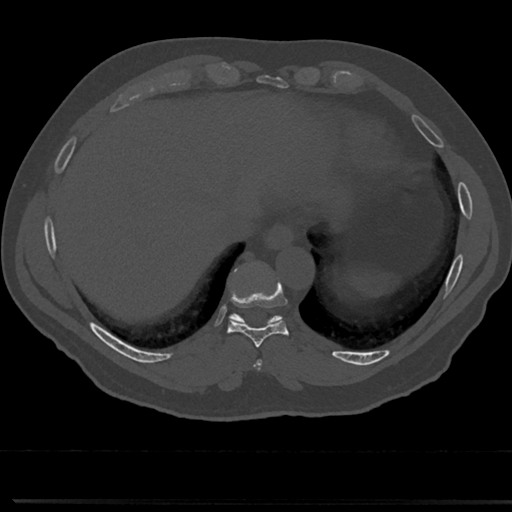
CT including the spine, one axial slice. Position 294 of 817 along the scan axis. Bone window (W 1800 / L 400 HU). 512 × 512 image matrix, field of view 355 × 355 mm. Patient: male, 61 years. Case-level facts recorded for this patient, not image findings: primary cancer: prostate.
Structures marked on this image (semi-automatically segmented with operator editing):
- T8 vertebra: bounding box [x1, y1, x2, y2] px = [251, 329, 278, 360]
- T9 vertebra: [217, 266, 295, 349]